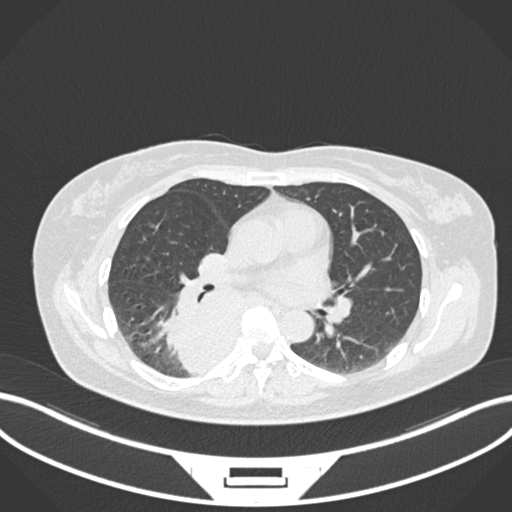
Chest CT, one axial slice. Slice 594 of 677 in the series (ordered by position). Reconstruction kernel B30f. 120 kVp. Lung window (W 1500 / L -600 HU). 1 mm slice thickness. 512 × 512 image matrix. Female patient, age 54 years. Case-level facts recorded for this patient, not image findings: clinical TNM (as recorded): T4 N0 M0.
Structures marked on this image (bounding box drawn by a radiologist):
- lung tumour (recorded histology: adenocarcinoma): bounding box (x1, y1, x2, y2) in pixels: (167, 281, 243, 377)